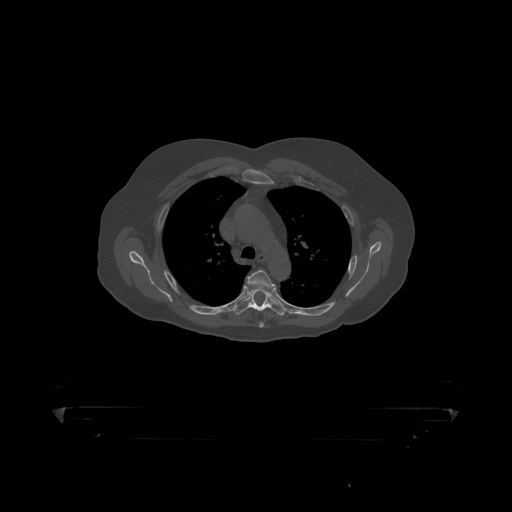
CT including the spine, one axial slice; position 328 of 390 along the scan axis; bone window (W 1800 / L 400 HU); 512 × 512 image matrix, field of view 650 × 650 mm. Male patient, age 60 years. From the clinical record (not read from this slice): primary cancer: prostate.
Annotated regions visible in this slice (semi-automatic segmentation, software-assisted and operator-edited):
- T4 vertebra: bounding box (x1, y1, x2, y2) in pixels: (246, 270, 276, 291)
- T5 vertebra: (233, 288, 287, 316)